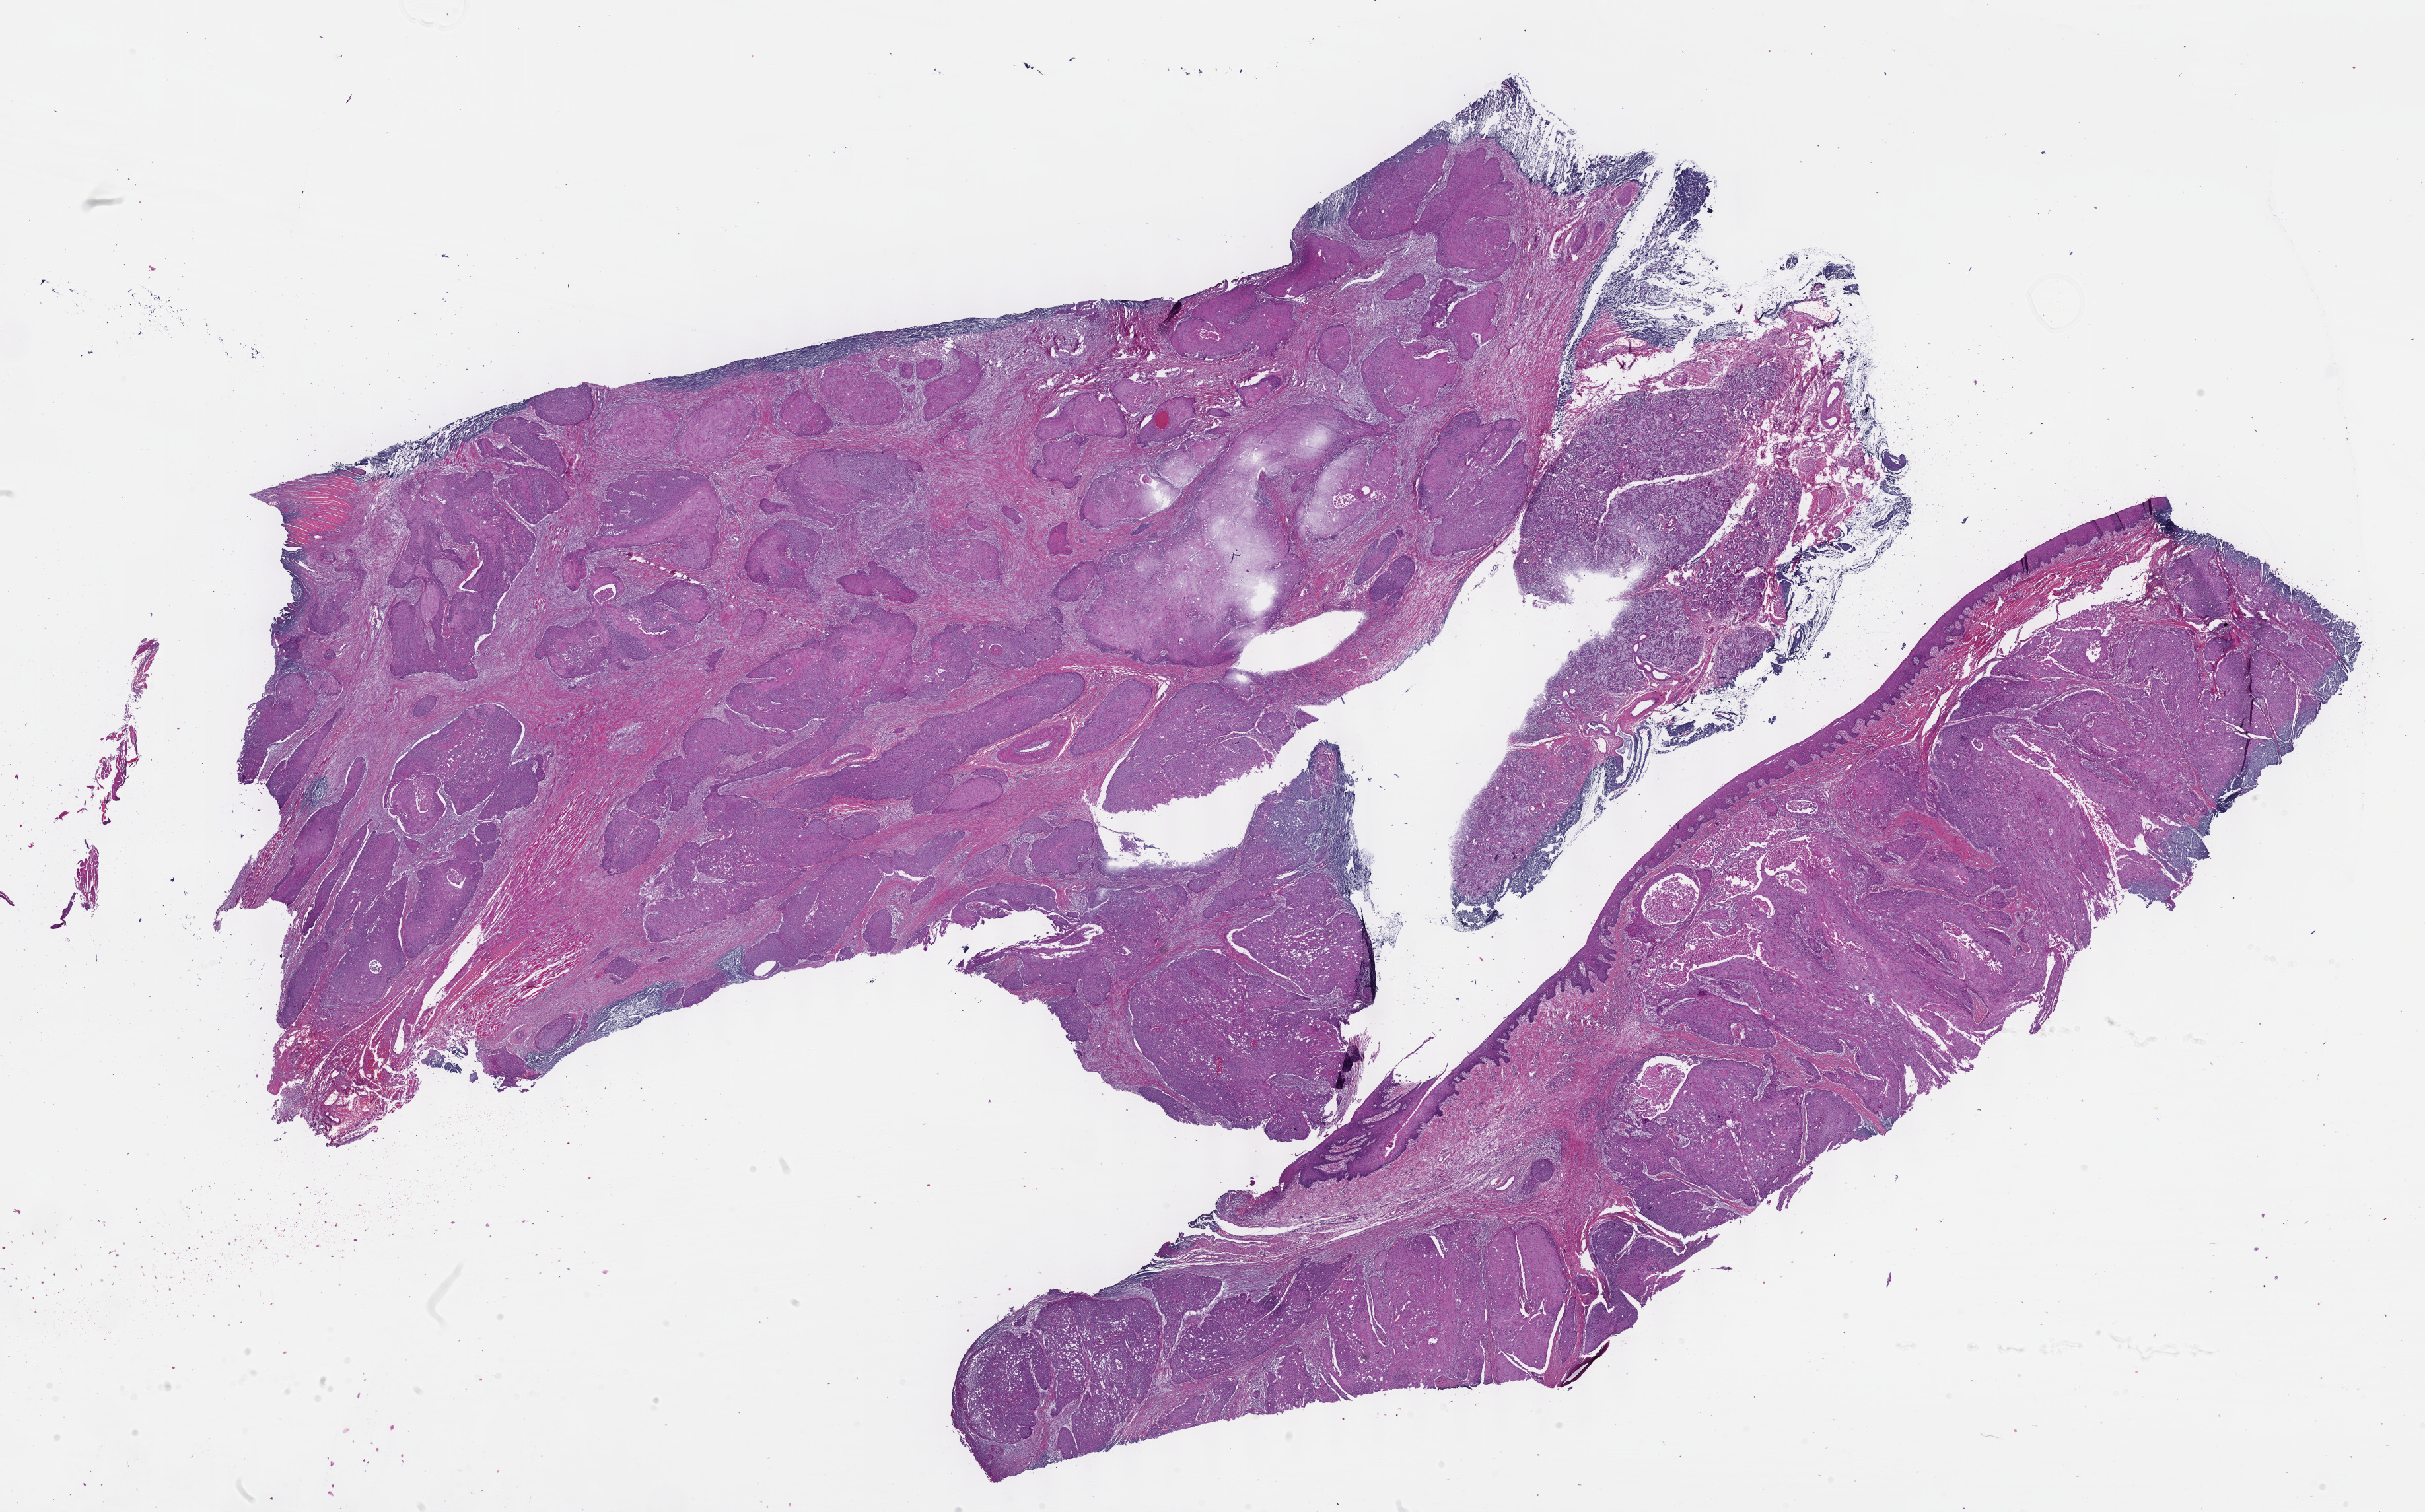
Whole-slide histology image, H&E-stained, shown as a low-resolution overview of the whole scanned area (about 29.7 x 18.5 mm). FFPE section. Primary tumour sample from the head and neck. Male, age 78 years at initial diagnosis. Histologic grade: G2 (moderately differentiated).
- histologic diagnosis: Squamous cell carcinoma, NOS (overlapping lesion of lip, oral cavity and pharynx)
- AJCC pathologic stage: IVA (7th edition)